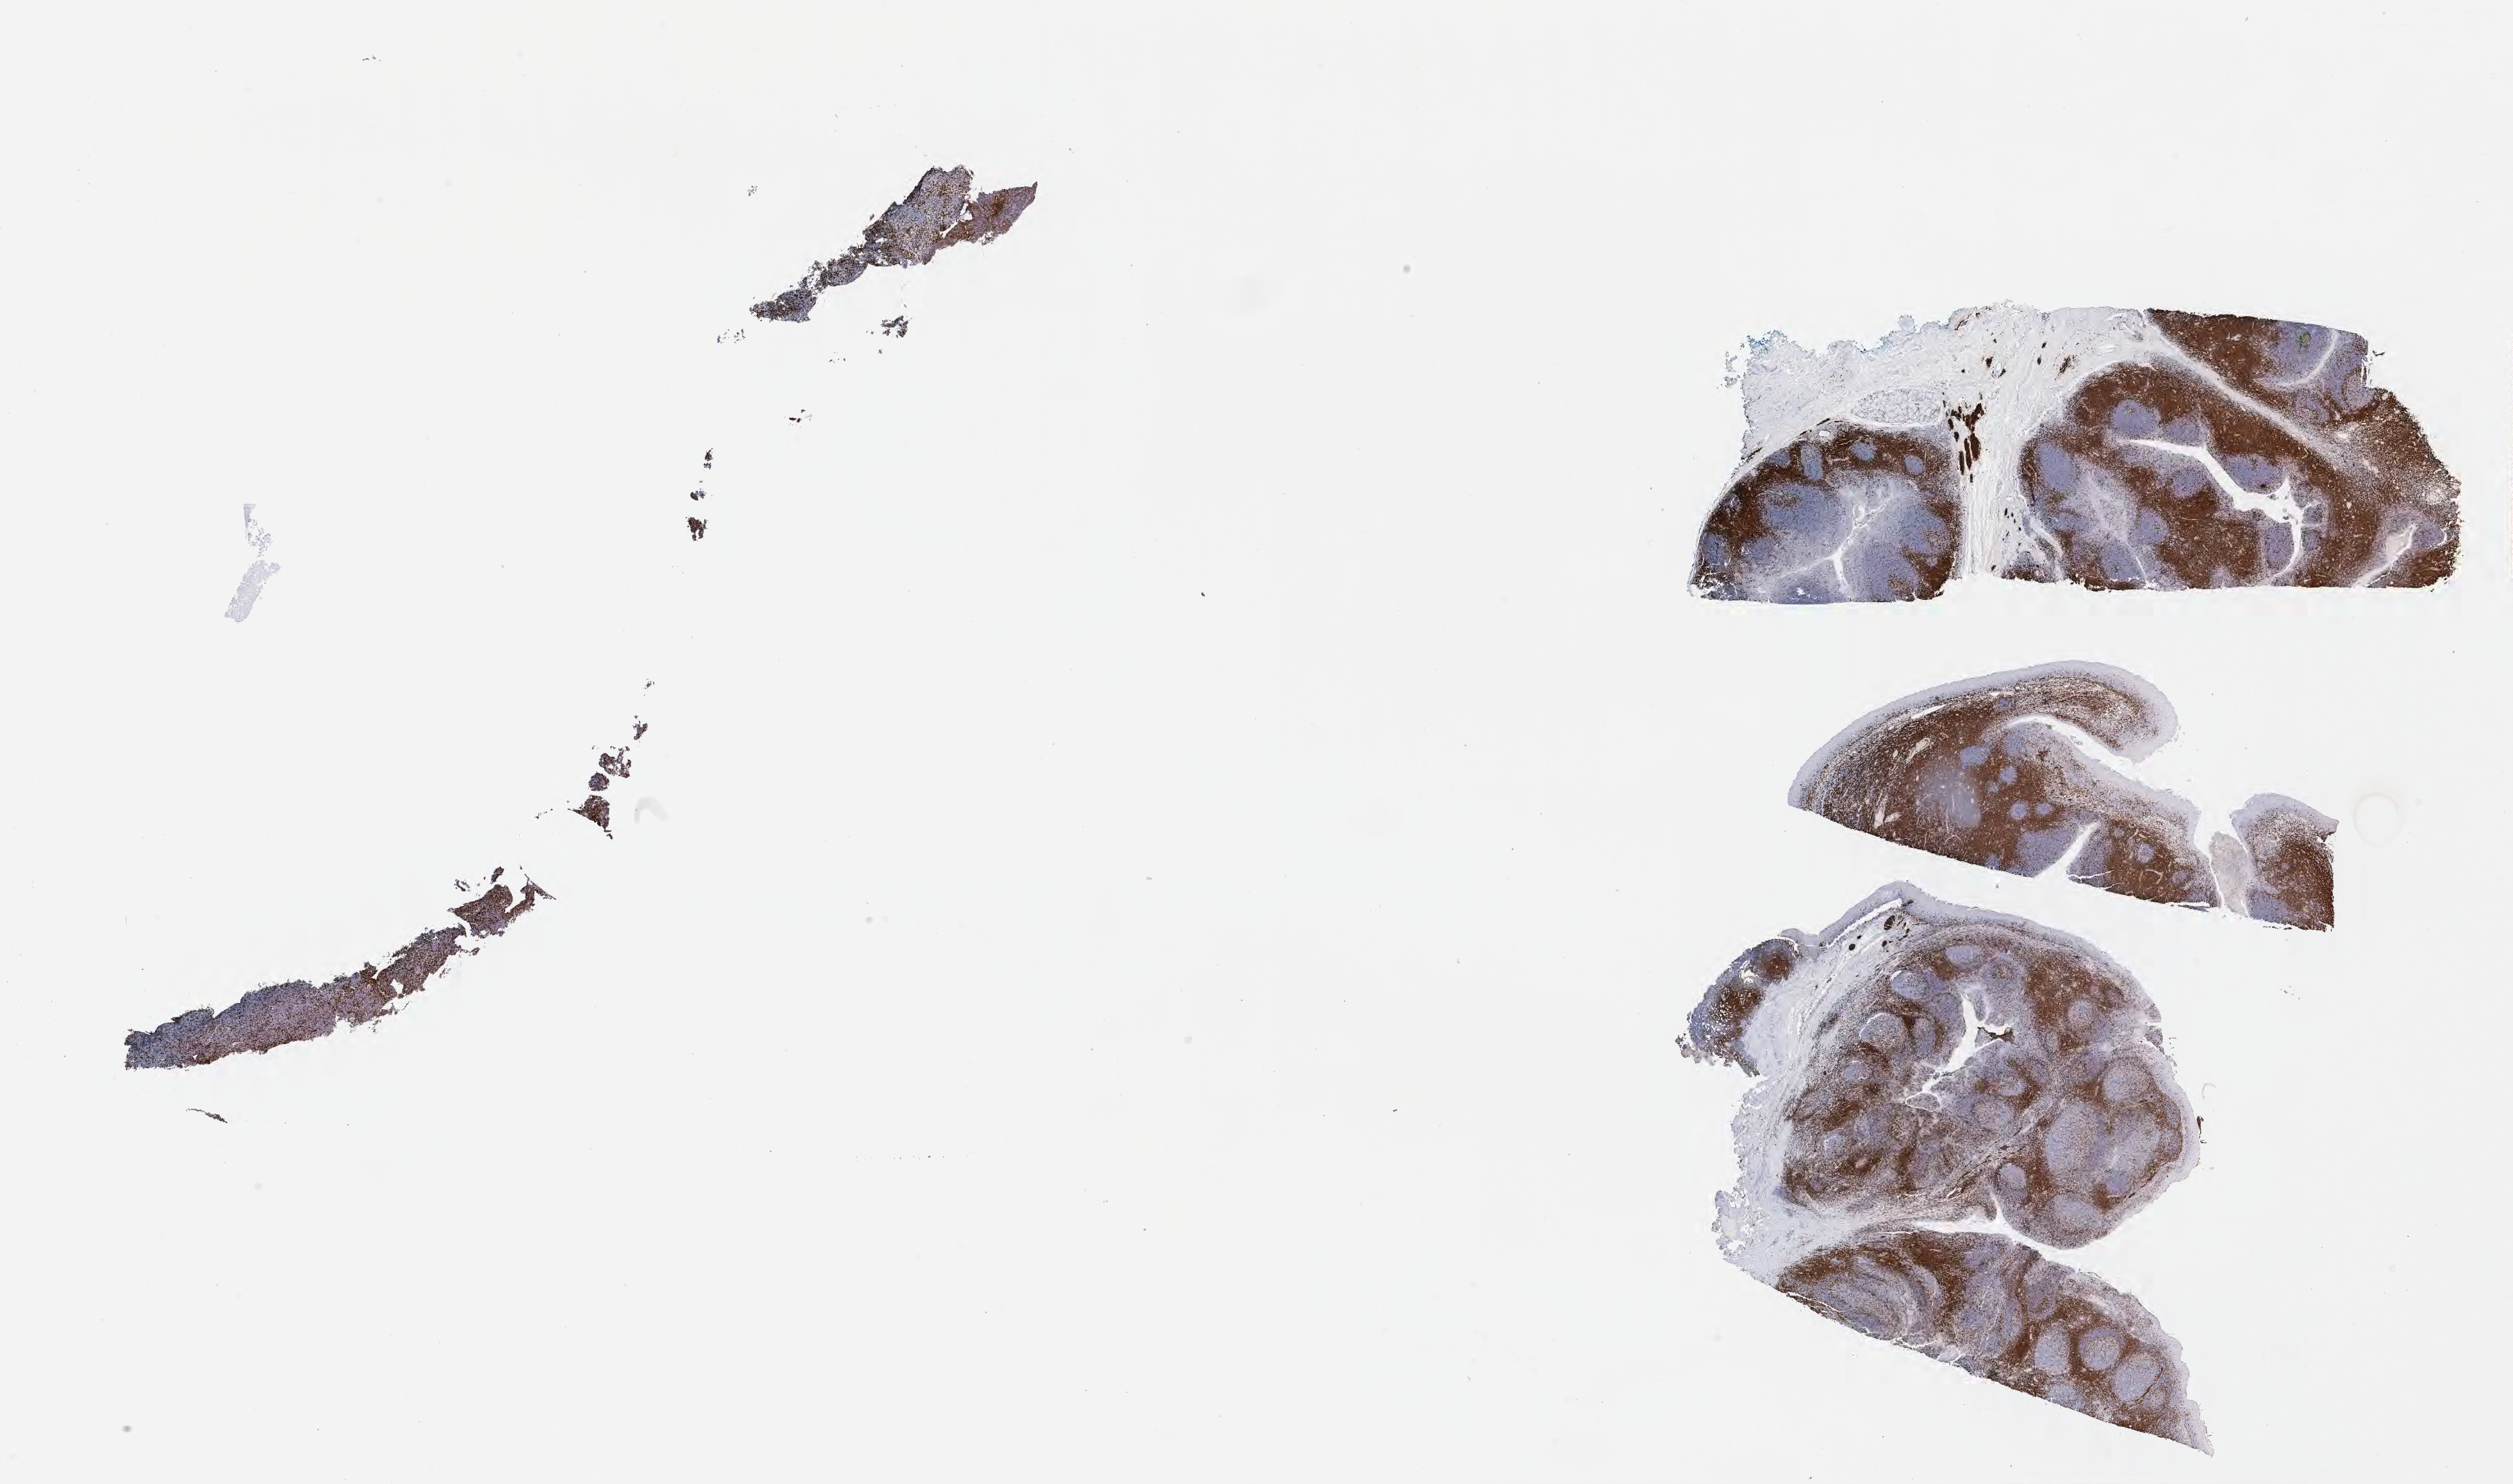
Immunohistochemistry (IHC) whole-slide image stained for CD3 — a low-resolution overview of the entire scanned area, about 31.7 x 18.7 mm, specimen: tumor tissue, anatomic site: cranium. Female patient; age at initial diagnosis 7 years.
* histologic diagnosis: Burkitt lymphoma, NOS